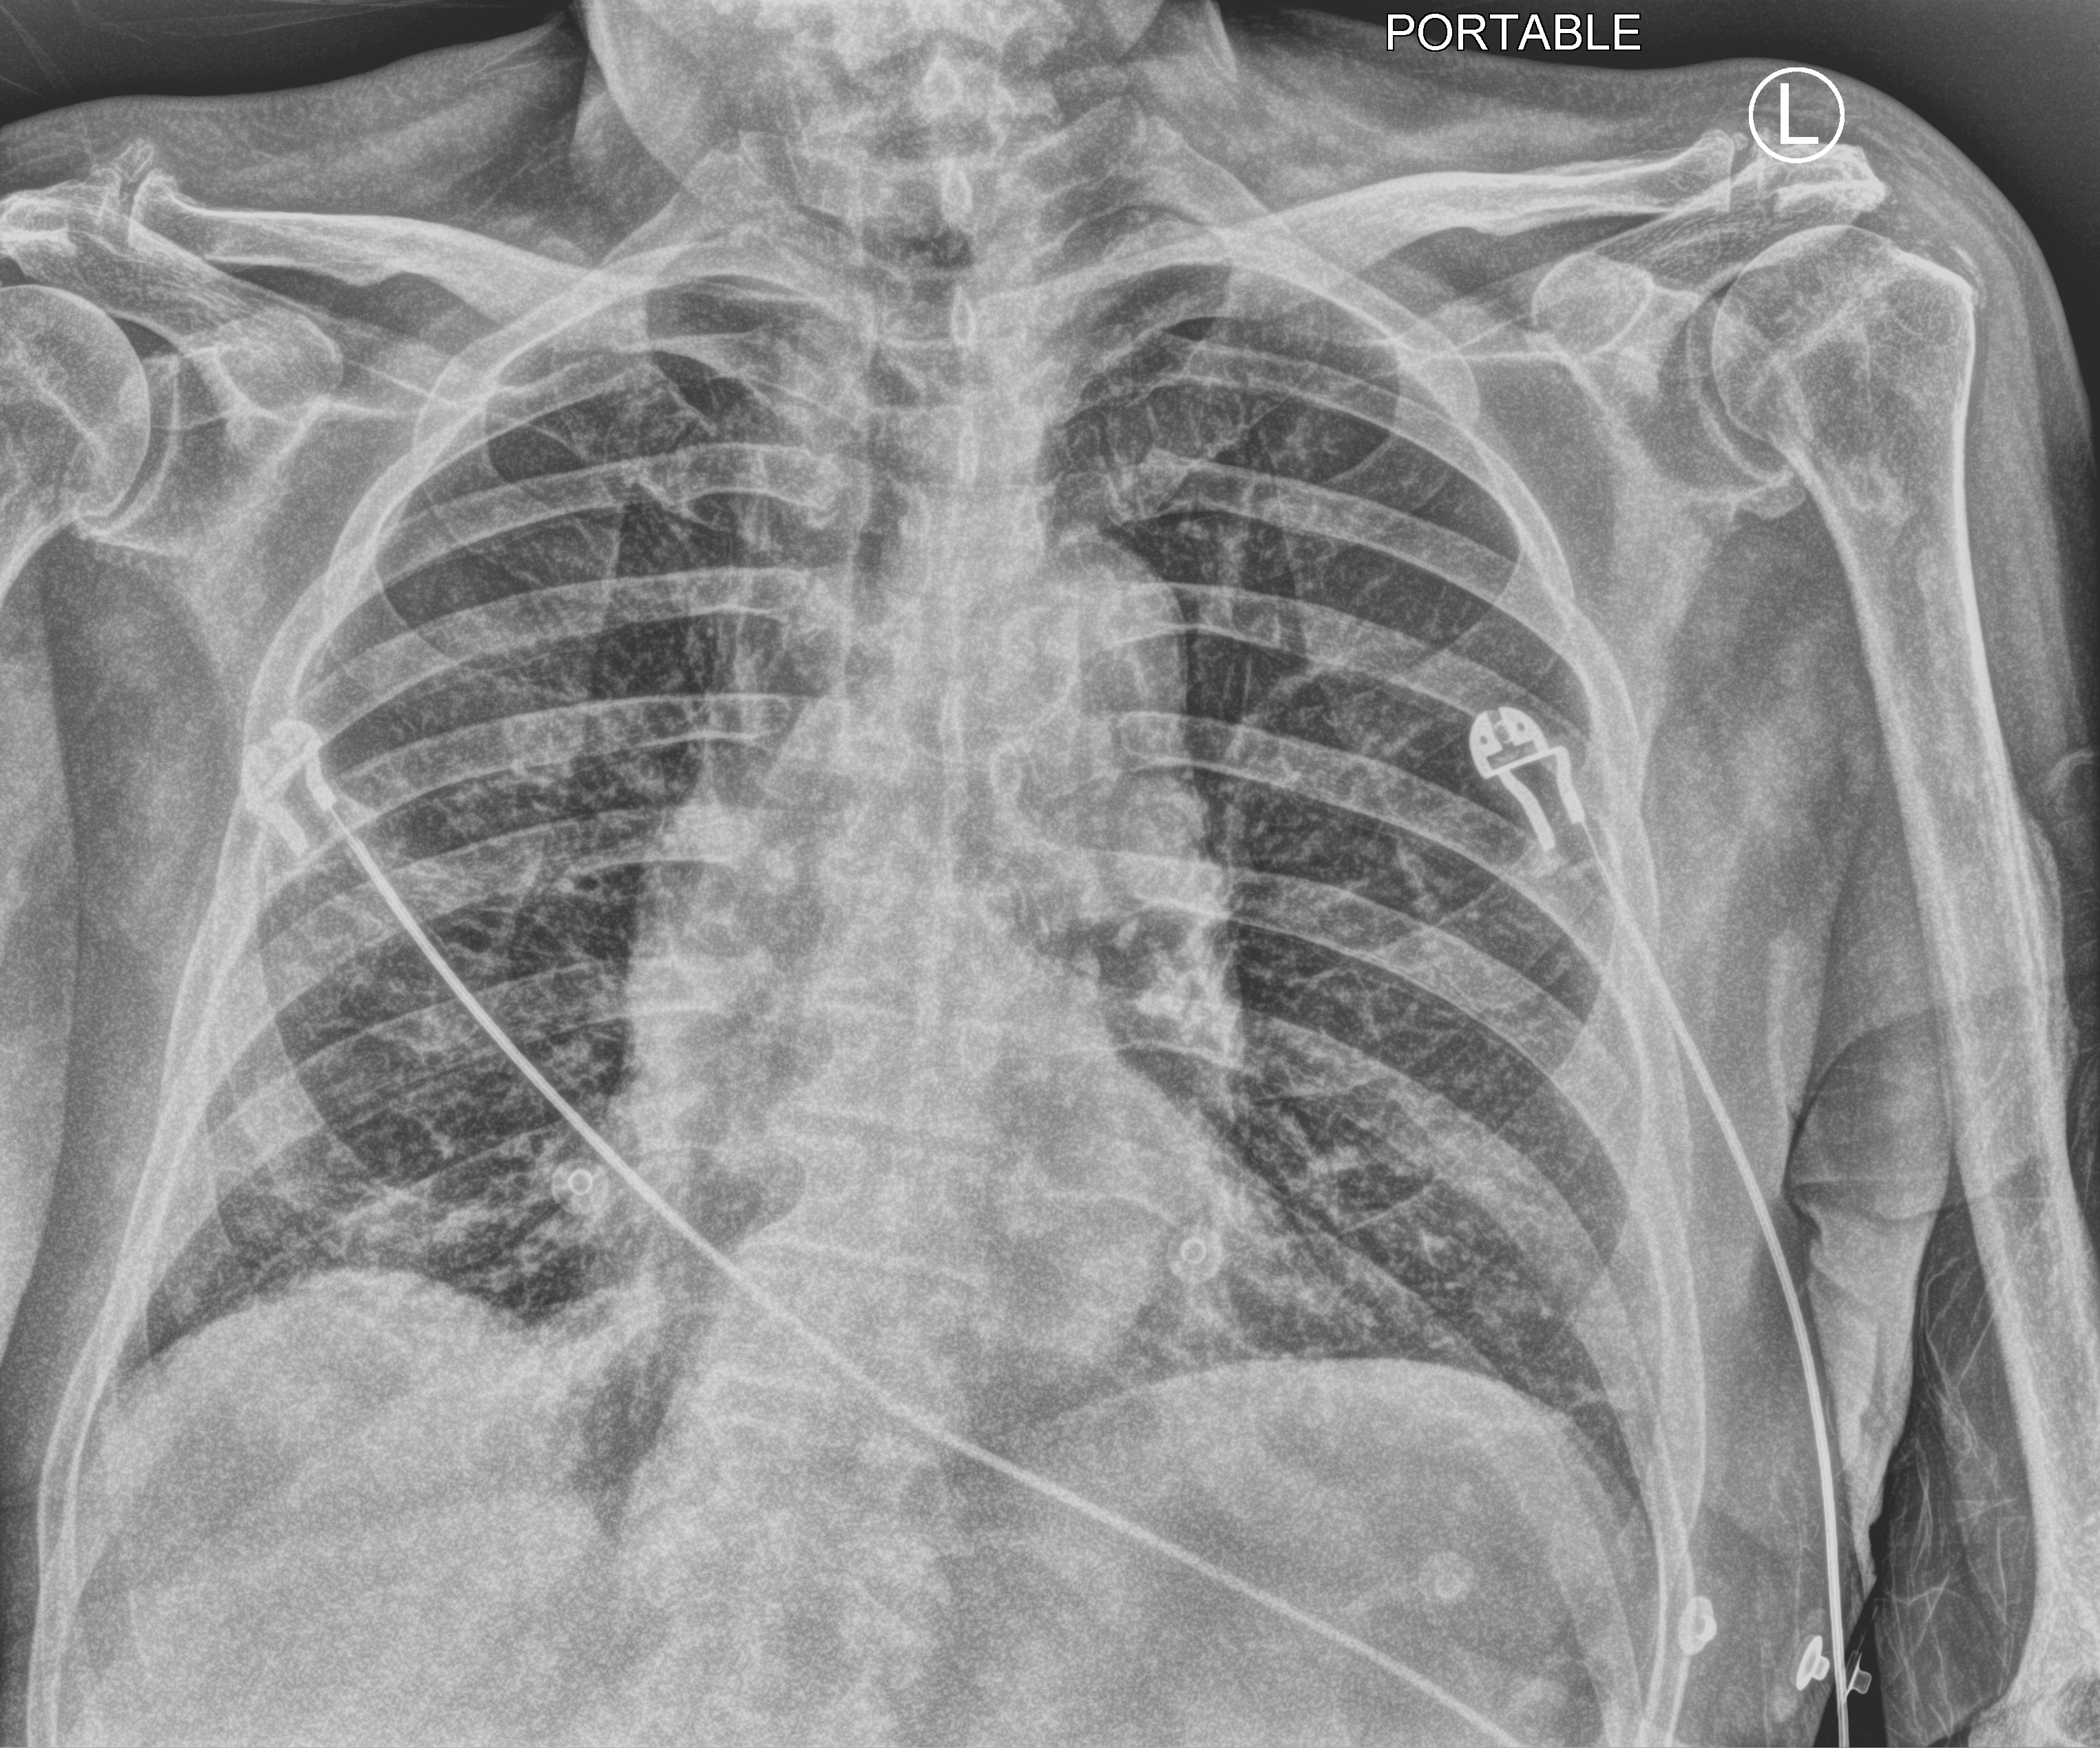
Bedside chest radiograph (computed radiography); anteroposterior (AP) projection. Patient hospitalised with COVID-19; male, aged 75–90 years.
From the hospital-stay record, not from the radiograph (when in the stay this image was taken is not recorded): mechanically ventilated during this hospital stay: no; length of hospital stay: 6 days; admitted to intensive care during this hospital stay: no.